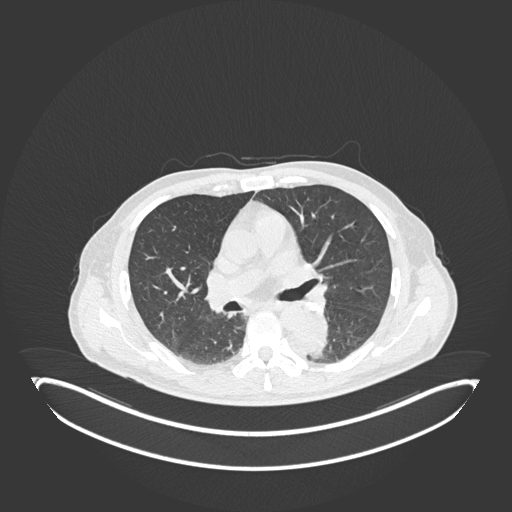
Chest CT, one axial slice. Position 118 of 251 along the scan axis. Reconstruction kernel B30f. 120 kVp. Lung window (W 1500 / L -600 HU). 1 mm slice thickness. 512 × 512 image matrix. Patient: male, 72 years. From the clinical record (not read from this slice): clinical TNM (as recorded): T2b N0 M1.
Outlined on this slice (rectangle marked by the reading radiologist):
- lung tumour (recorded histology: adenocarcinoma): bounding box (x1, y1, x2, y2) in pixels: (299, 316, 333, 362)